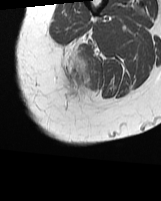
MRI of an extremity soft-tissue mass, one axial slice. Position 11 of 70 along the scan axis. MR volume resampled by the dataset authors to the PET/CT grid (not the native acquisition matrix). 3.27 mm slice thickness. 161 × 201 image matrix, field of view 157 × 196 mm. Female patient. From the clinical record (not read from this slice): histological type: synovial sarcoma; grade: intermediate; site of the primary tumour: right buttock.
Outlined on this slice (expert contour drawn on MRI and transferred to this co-registered scan by the dataset authors):
- gross tumour volume including surrounding oedema: bounding box (x1, y1, x2, y2) in pixels: (63, 47, 91, 96)